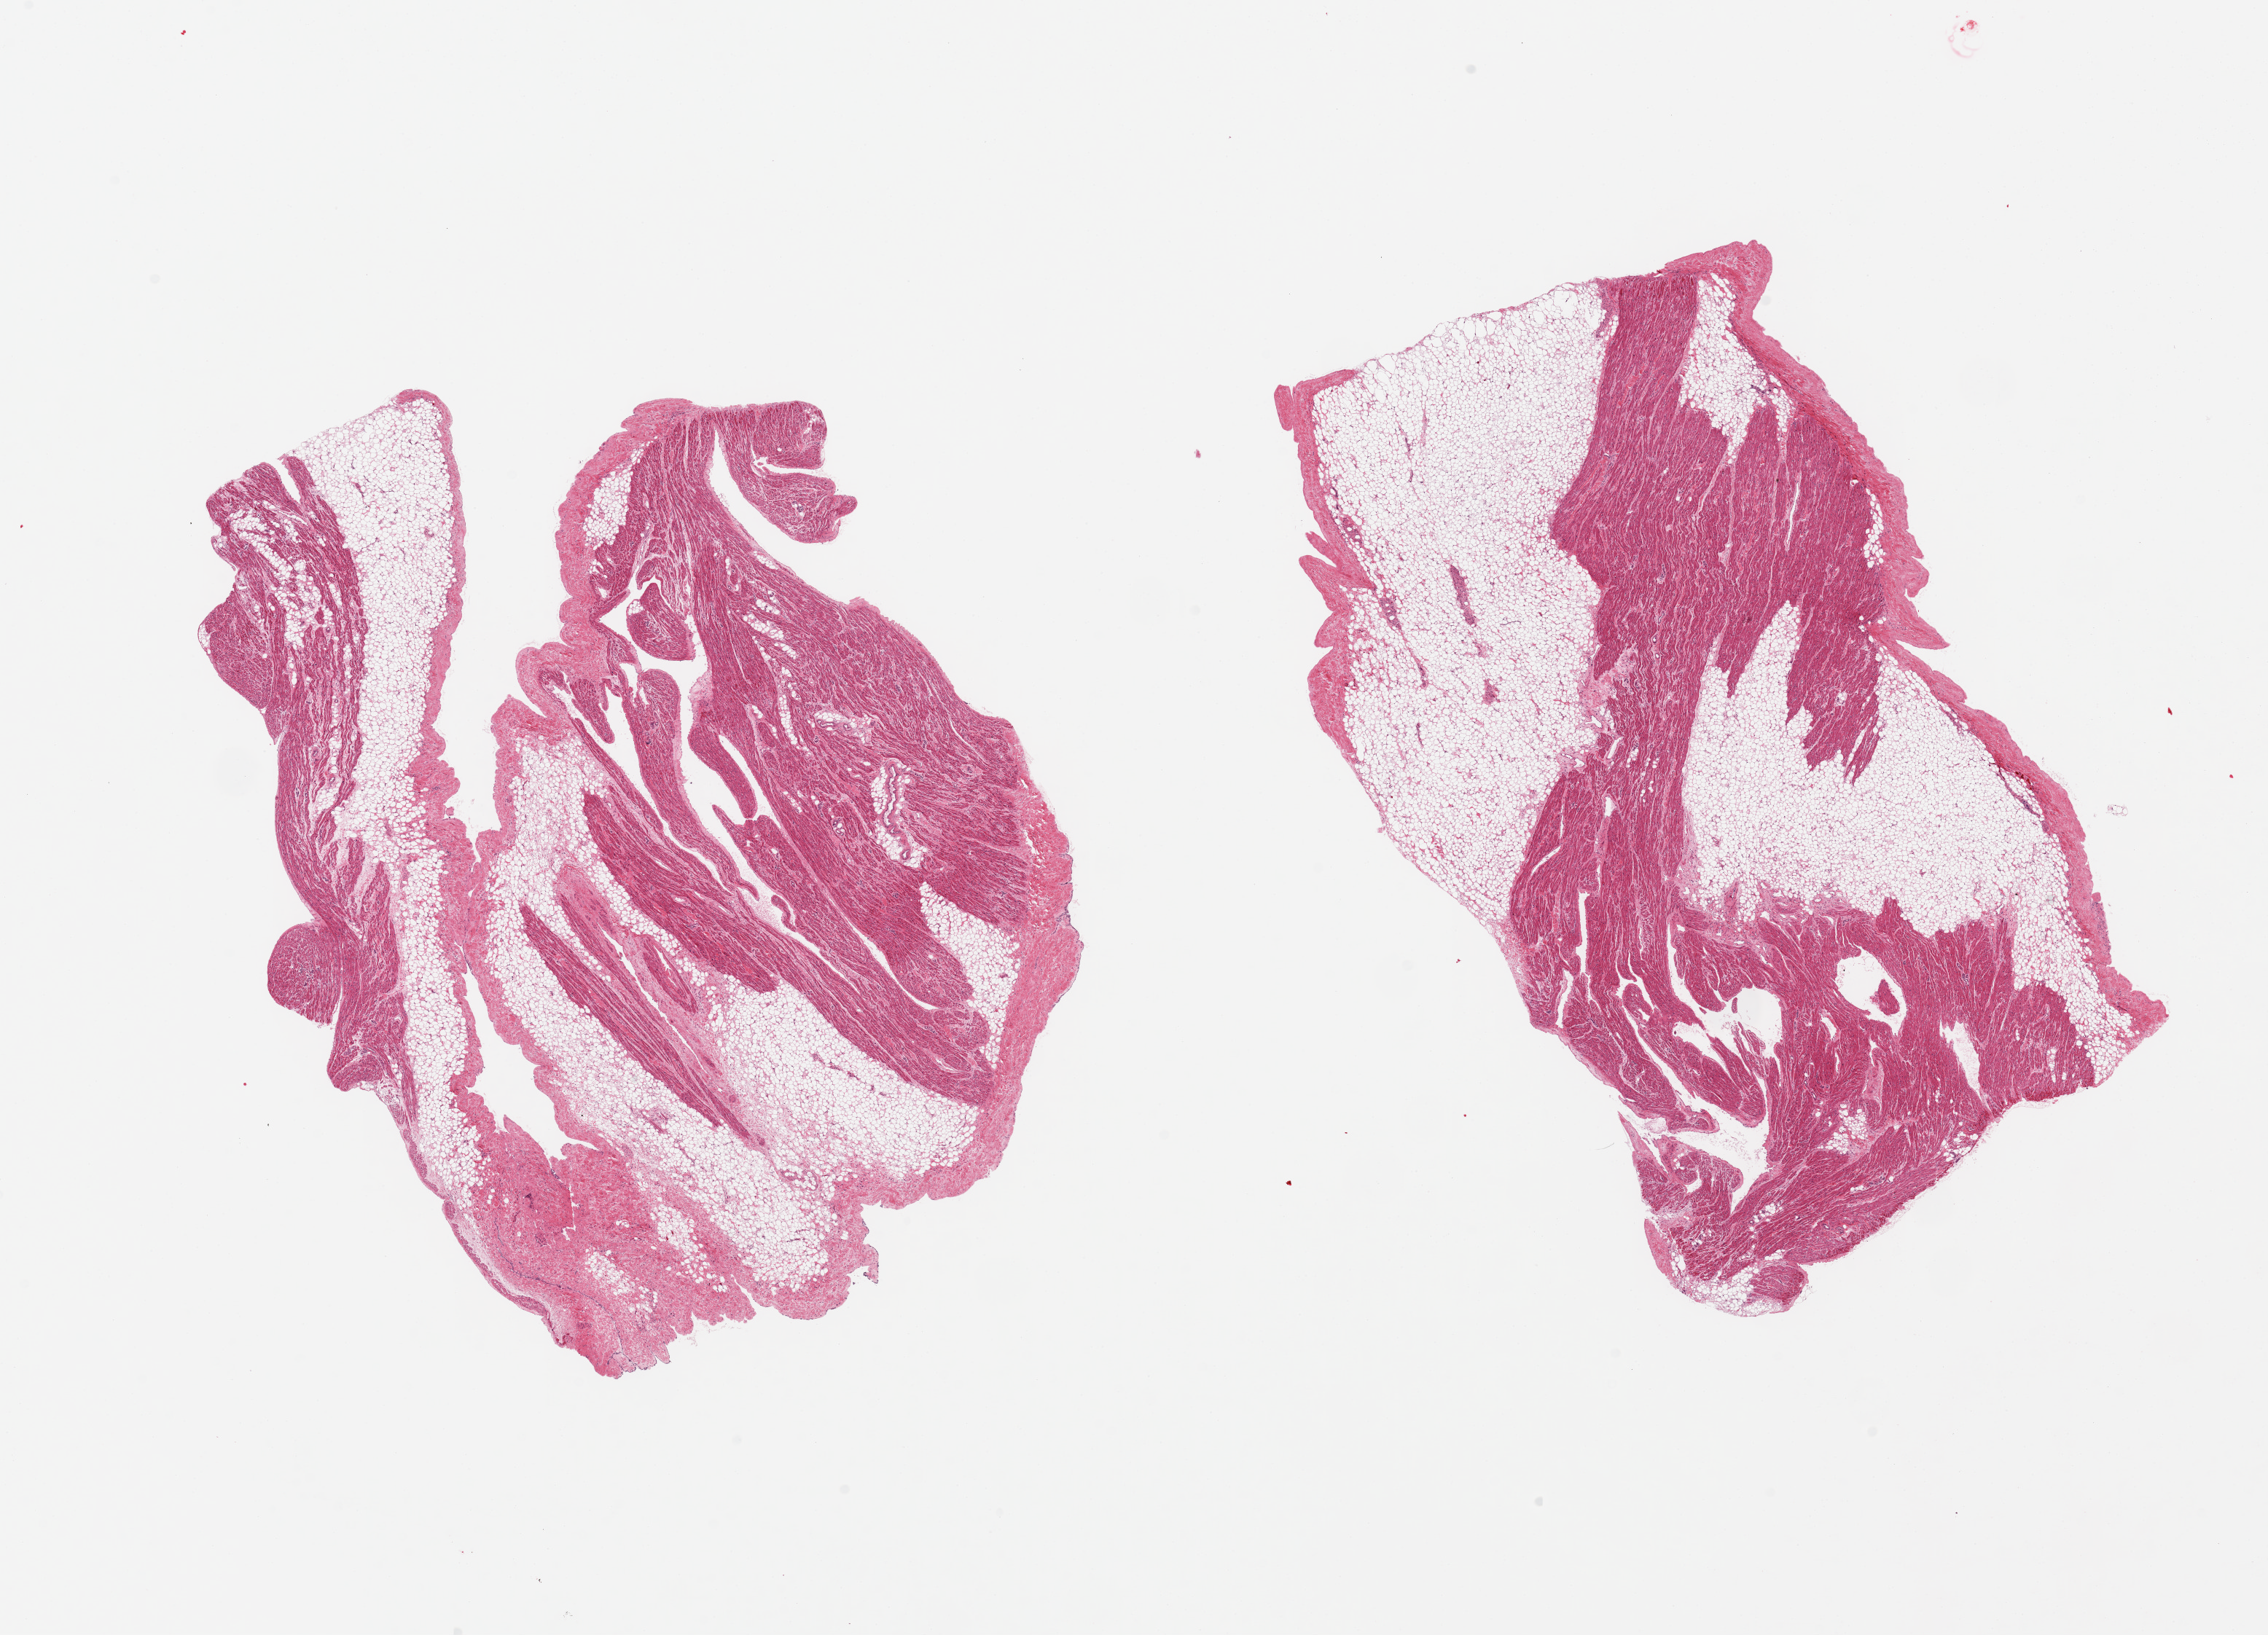
Whole-slide image, haematoxylin and eosin stain, whole scanned area (about 24.6 x 17.7 mm) shown as a low-resolution overview; PAXgene-fixed, paraffin-embedded tissue; section of auricular appendage (target tissue); donor tissue sample. Female donor.
- reviewer comment on this tissue sample: 2 pieces, ~40% fat